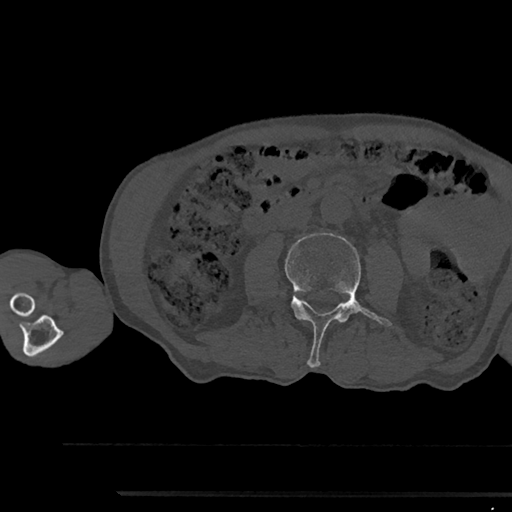
CT including the spine, one axial slice. Slice 485 of 797 in the series (ordered by position). Reconstruction kernel Br40s/3. Bone window (W 1800 / L 400 HU). 512 × 512 image matrix, field of view 367 × 367 mm. Male patient, age 79 years. From the clinical record (not read from this slice): primary cancer: prostate.
Outlined on this slice (semi-automatic segmentation, software-assisted and operator-edited):
- L3 vertebra: bounding box (x1, y1, x2, y2) in pixels: (285, 233, 391, 367)